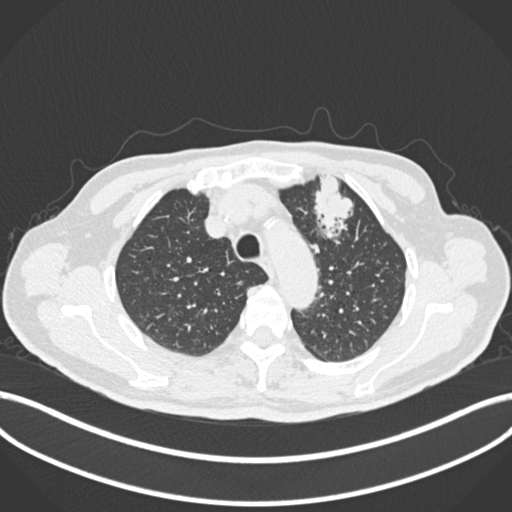
Chest CT, one axial slice; slice 203 of 261 in the series (ordered by position); reconstruction kernel B30f; 120 kVp; lung window (W 1500 / L -600 HU); 512 × 512 image matrix, field of view 400 × 400 mm. Patient: male, 74 years. Case-level facts recorded for this patient, not image findings: clinical TNM (as recorded): T2b N0 M1c.
Annotated regions visible in this slice (bounding box drawn by a radiologist):
- lung tumour (recorded histology: adenocarcinoma): bounding box (x1, y1, x2, y2) in pixels: (311, 173, 358, 243)